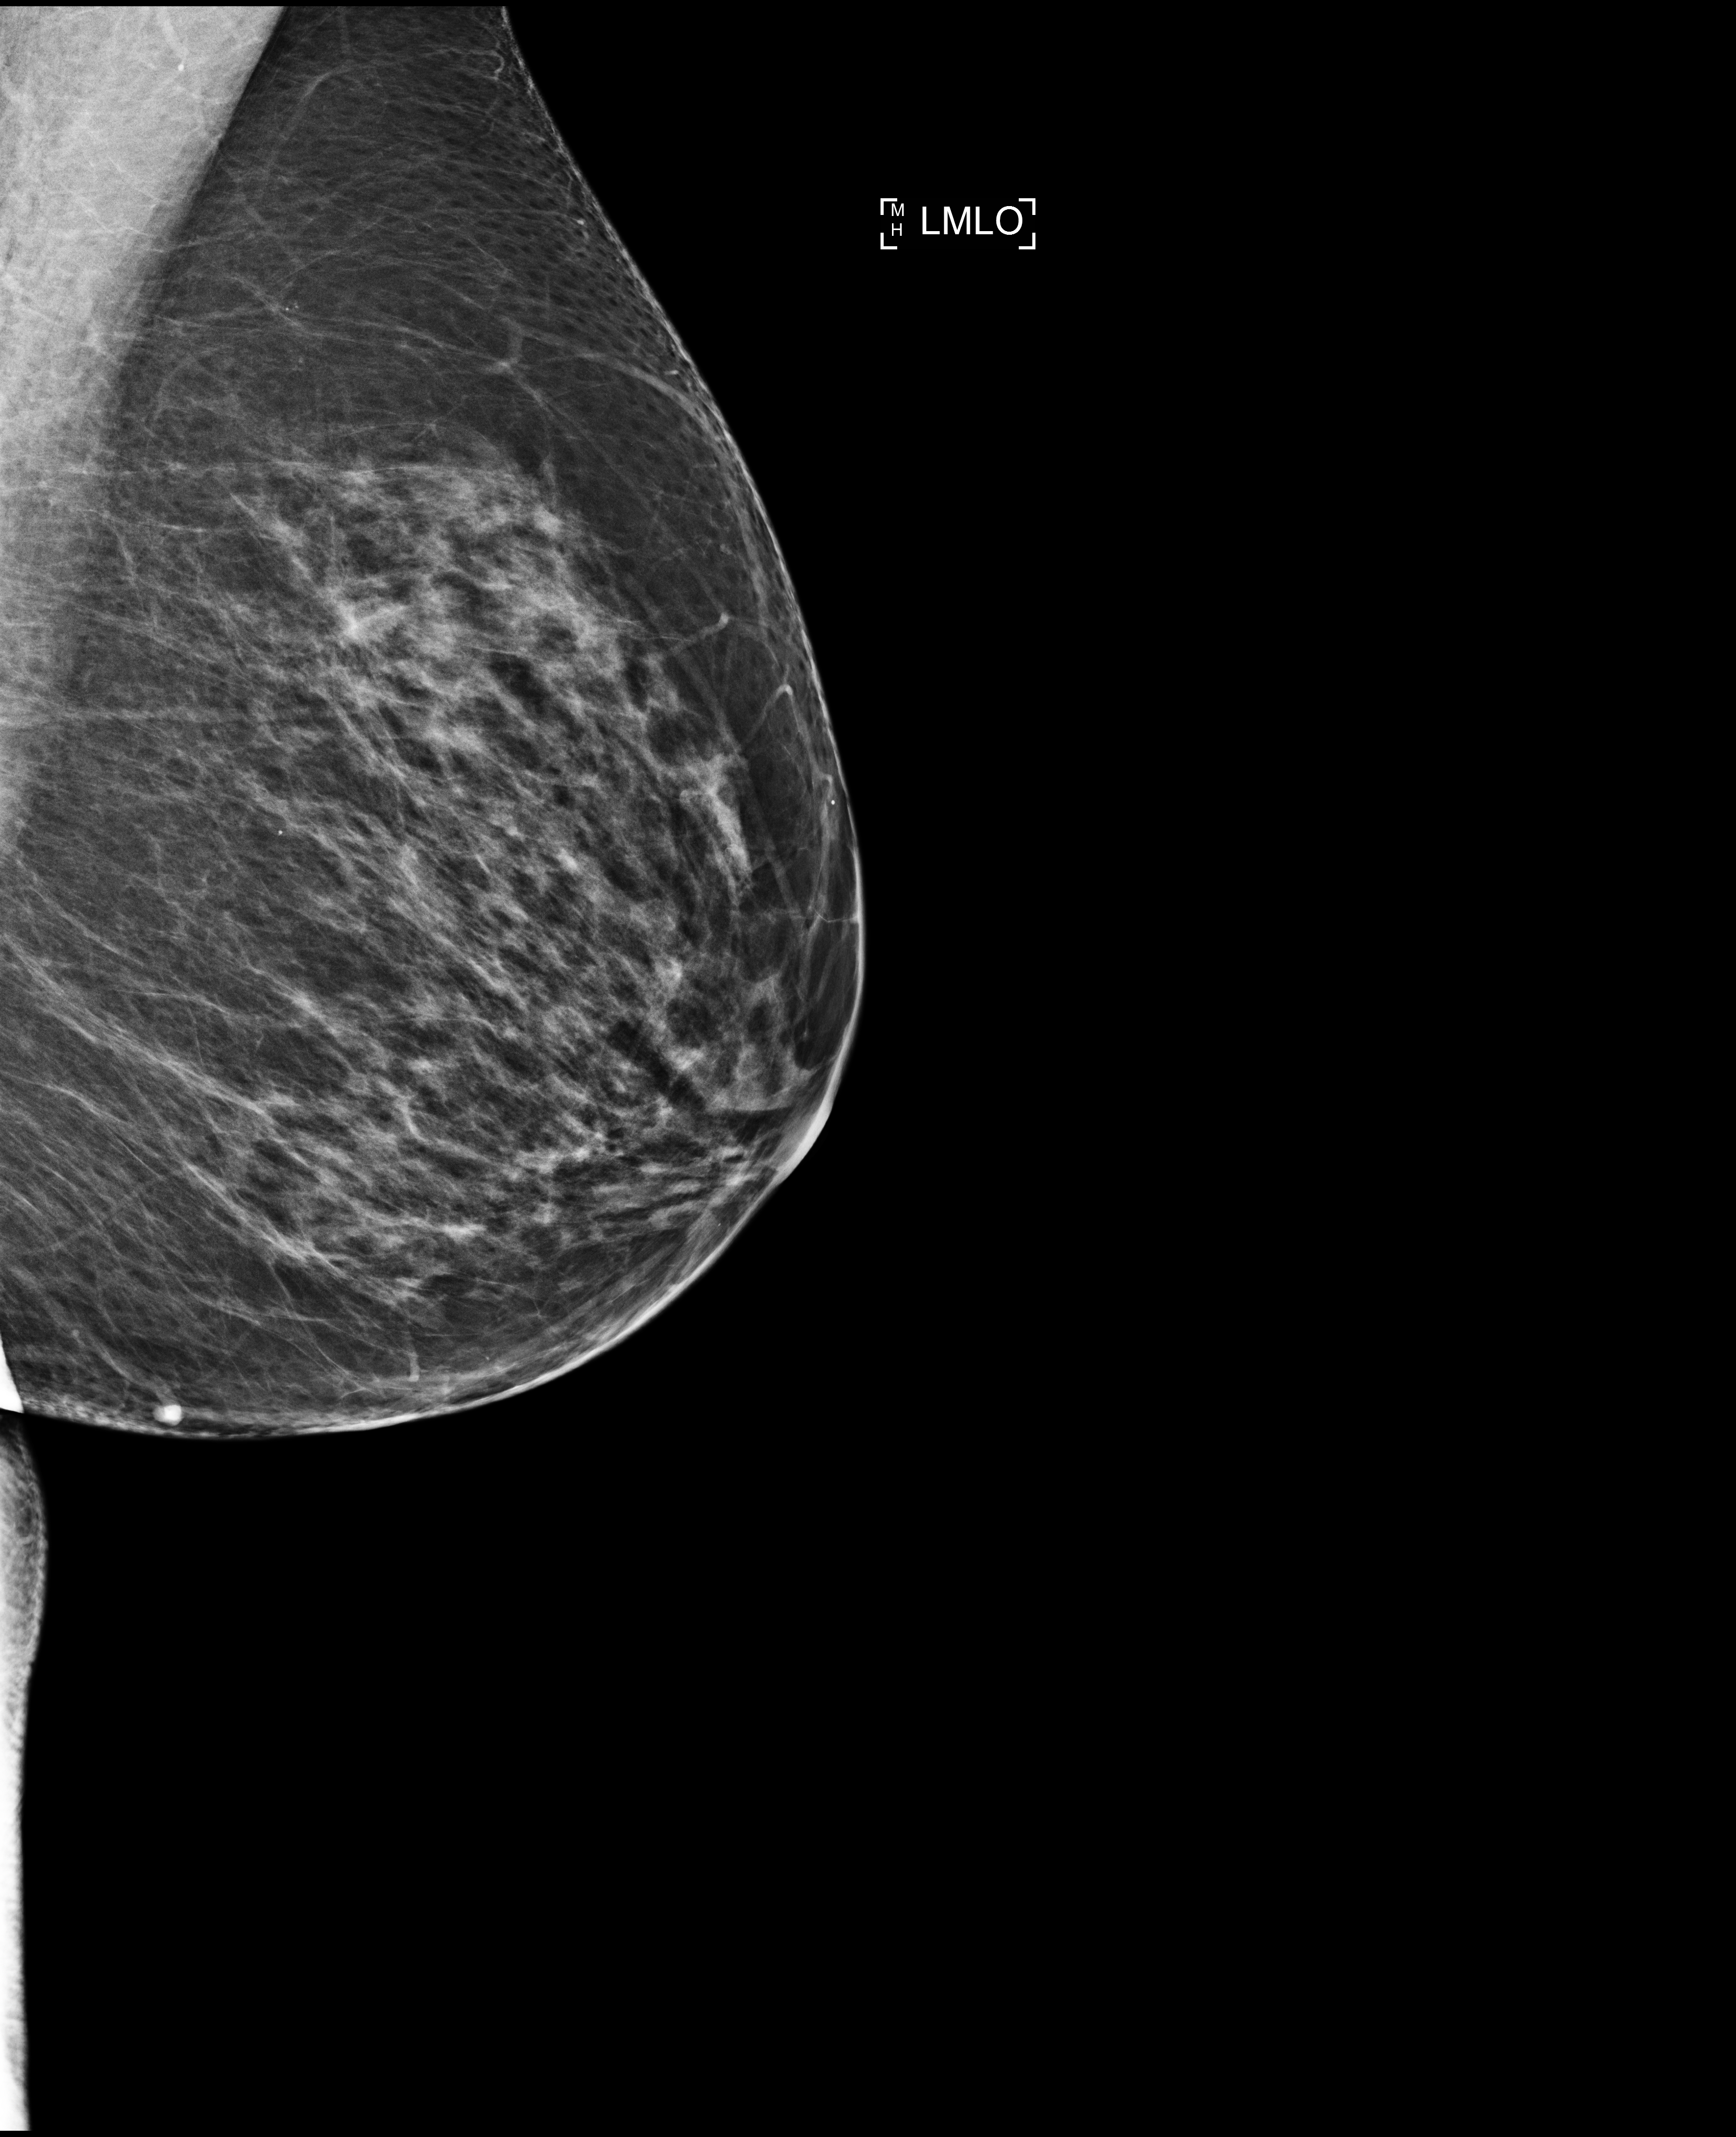
Full-field digital mammogram (FFDM); left breast; medio-lateral oblique projection; screening examination; compressed breast thickness 68 mm. Female patient, age 70 years.
BI-RADS breast density category at the screening exam (both breasts, scale 1–4): 2. Final BI-RADS category for the screening round (tomosynthesis exam, both breasts): category 1. Recall: no recall after this screen.